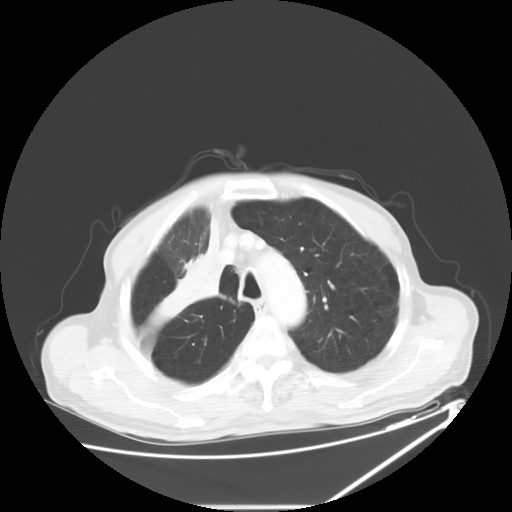
Chest CT, one axial slice. Slice 48 of 60 in the series (ordered by position). Reconstruction kernel STANDARD. 120 kVp. Lung window (W 1500 / L -600 HU). 5 mm slice thickness. 512 × 512 image matrix, field of view 410 × 410 mm. Male patient, age 73 years. From the clinical record (not read from this slice): clinical TNM (as recorded): T2a N1 M0.
Annotated regions visible in this slice (bounding box drawn by a radiologist):
- lung tumour (recorded histology: squamous cell carcinoma): bounding box (x1, y1, x2, y2) in pixels: (145, 204, 225, 322)